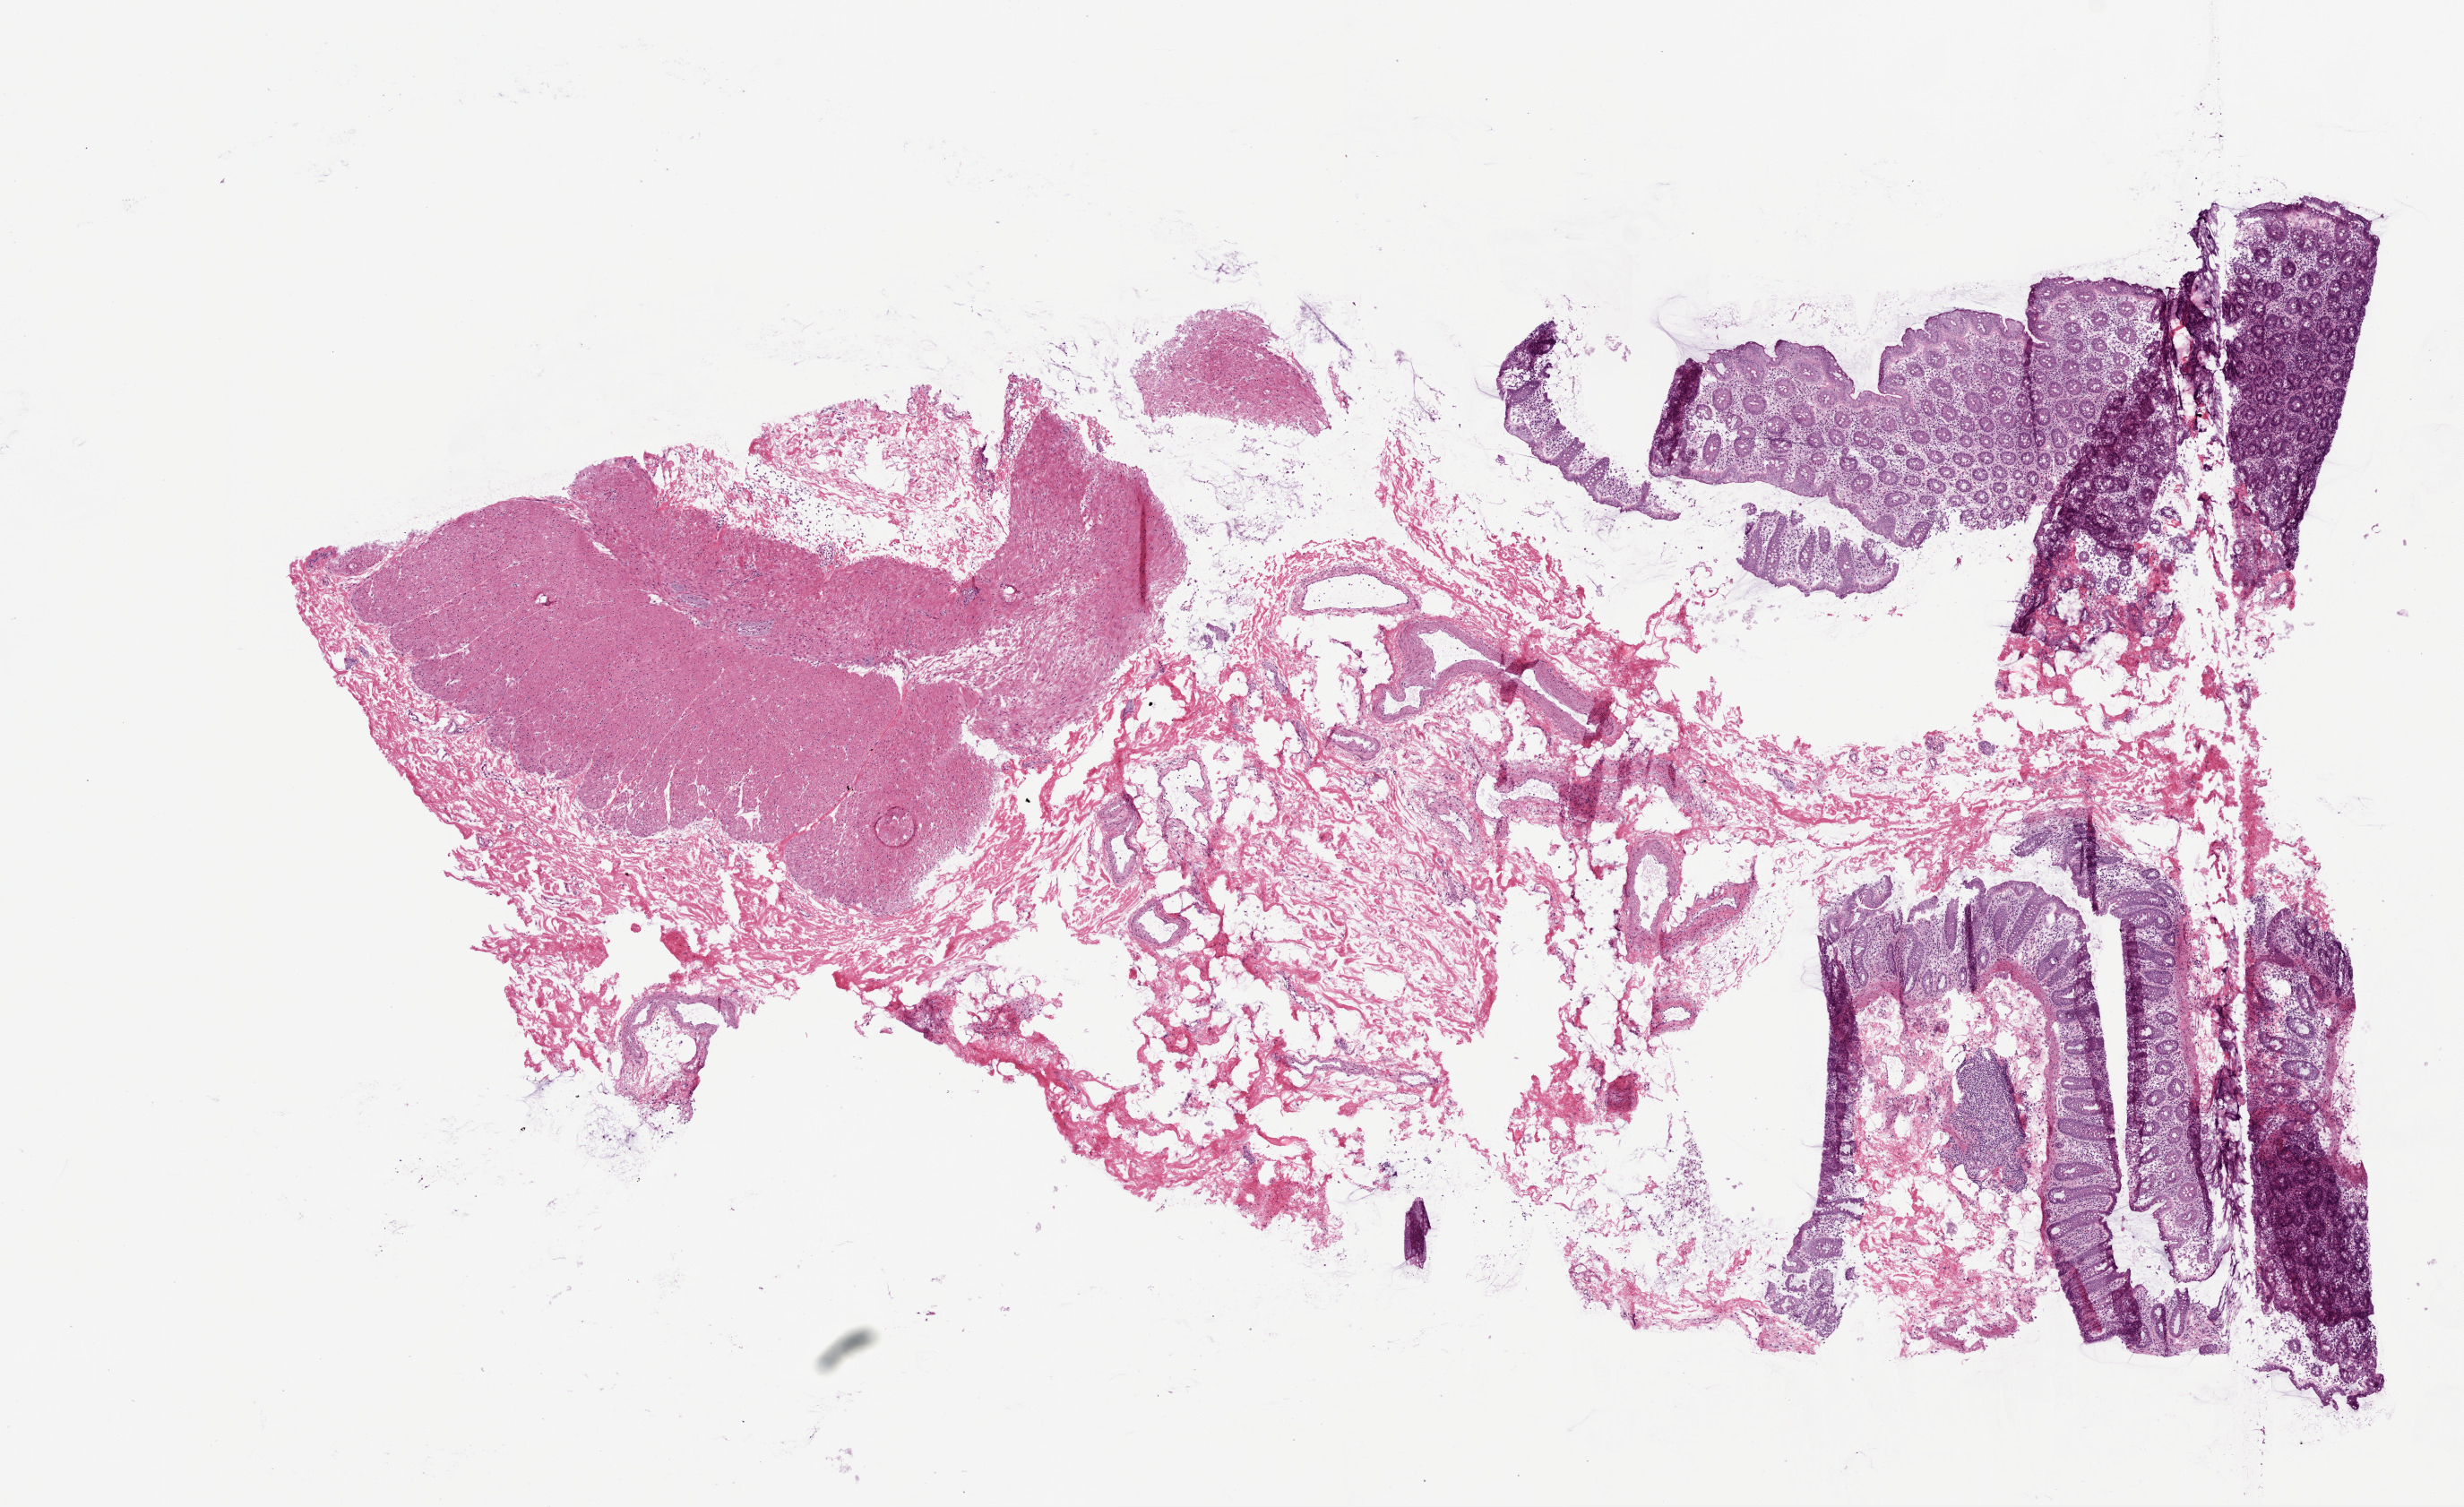
Digitized H&E-stained tissue section (whole slide), a low-resolution overview of the entire scanned area, about 11.0 x 6.7 mm (from a 20x scan); frozen section from the top of the tissue portion; solid tissue normal (non-tumour tissue) sample from the colon. Male, age 73 years at initial diagnosis.
This section: solid tissue normal (non-tumour) sample from the same patient. Patient diagnosis: Adenocarcinoma, NOS (ascending colon).